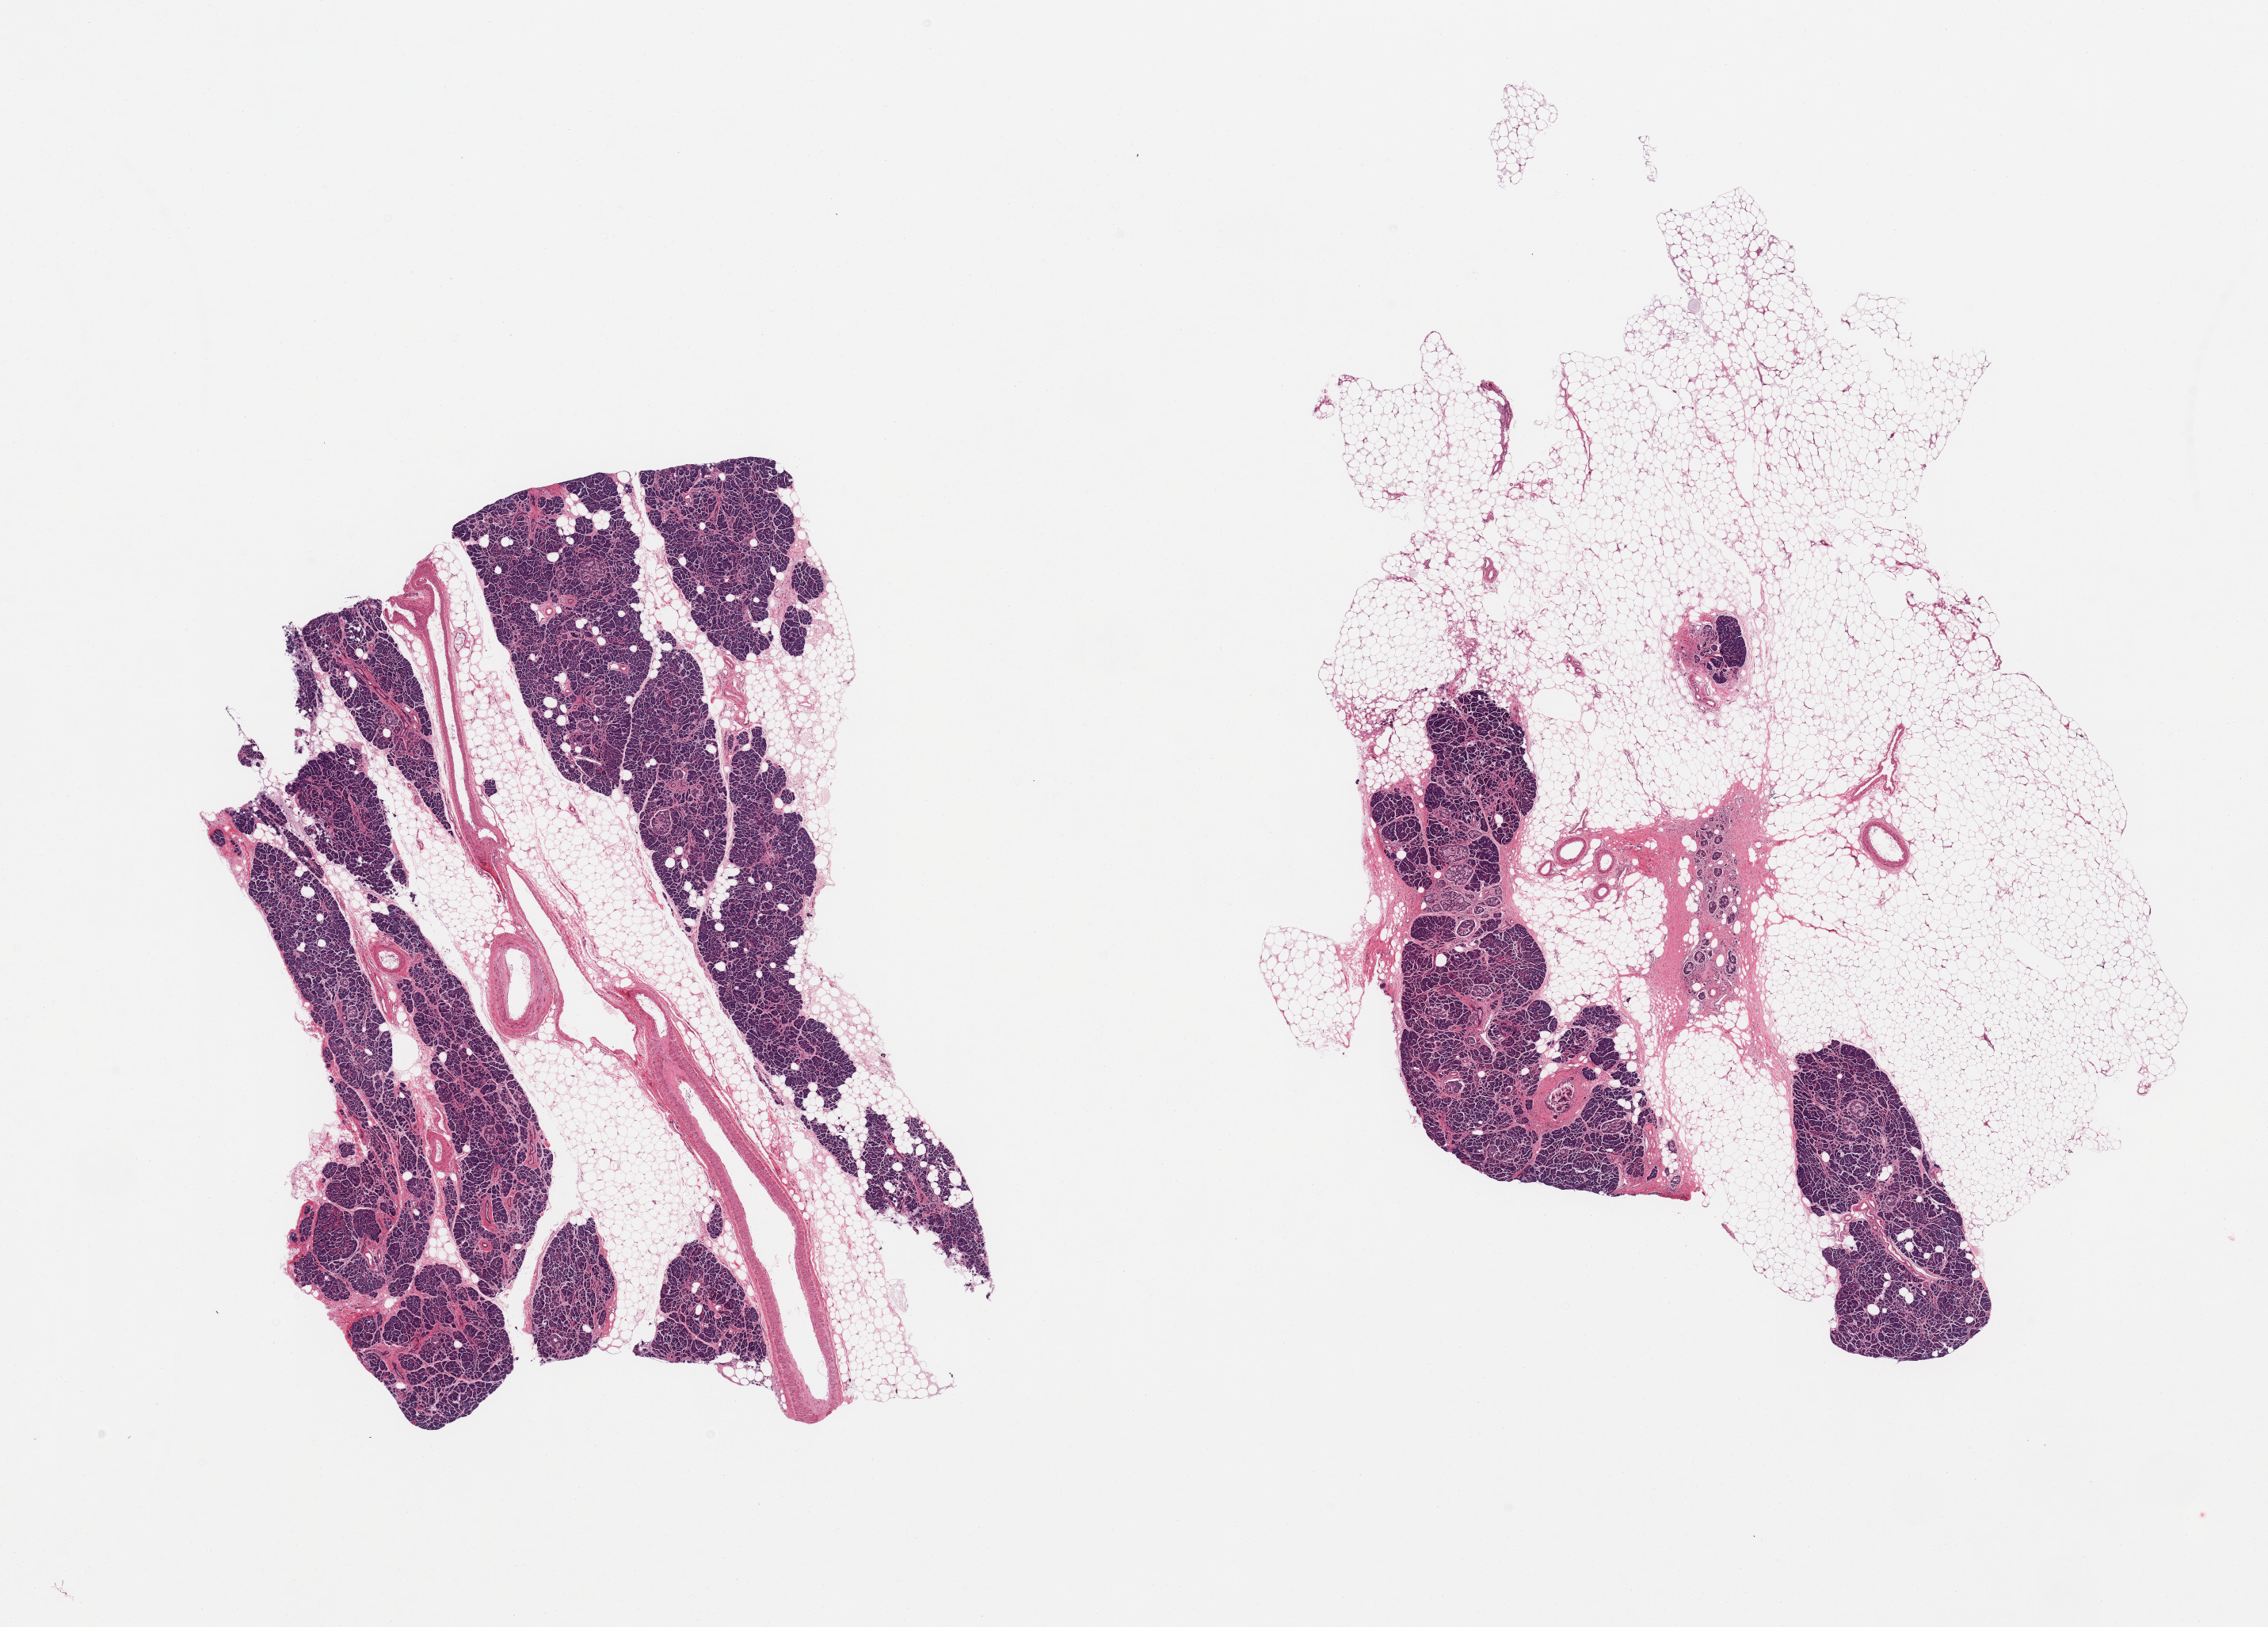
Digitized hematoxylin and eosin (H&E)-stained section, low-resolution overview of the scanned area, about 22.6 x 16.2 mm. PAXgene-fixed paraffin-embedded (PFPE) section. Target tissue: pancreas. Donor tissue sample. Donor sex: female.
- review note (as recorded): 2 pieces; acinar atrophy & focal fibrosis: 70% & 40% internal & external fat